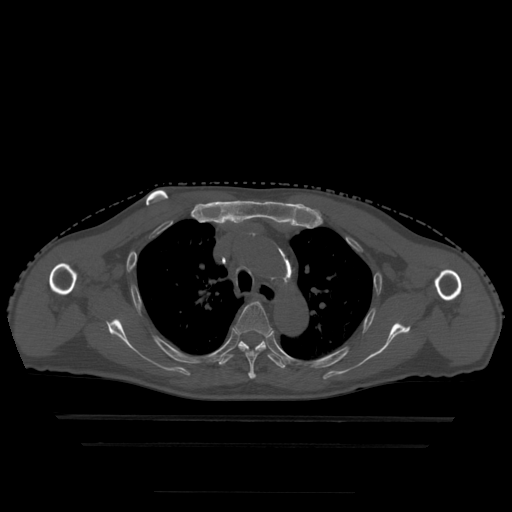
CT including the spine, one axial slice. Slice 348 of 522 in the series (ordered by position). Bone window (W 1800 / L 400 HU). 1.25 mm slice thickness. 512 × 512 image matrix. Patient age 68 years. Case-level facts recorded for this patient, not image findings: primary cancer: urothelial.
Outlined on this slice (semi-automatic segmentation, software-assisted and operator-edited):
- T4 vertebra: bounding box <234,302,272,379> (left, top, right, bottom; pixels)
- T5 vertebra: <219,340,286,369>